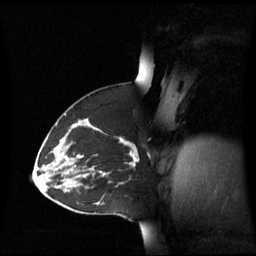
Breast MRI (dynamic contrast-enhanced), one sagittal slice. Slice 37 of 60 in the series (ordered by position). Dynamic contrast-enhanced series, image 2 of 3 at this slice position (ordered by acquisition). 1.5 T. TE 4.2 ms, TR 8.4 ms. 2.8 mm slice thickness. 256 × 256 image matrix, field of view 270 × 270 mm. Patient: female, 43 years. Case-level facts recorded for this patient, not image findings: setting: breast cancer imaged before/during neoadjuvant chemotherapy; receptor status: triple-negative.
Structures marked on this image (semi-automatically segmented with operator editing):
- analysis volume of interest (the breast-tissue region the enhancement analysis was run in; not a lesion): box from (x=55, y=124) to (x=139, y=173) px
- tumour enhancement mask (voxels above the 70 % enhancement threshold inside the analysis volume of interest): (x=58, y=137)–(x=139, y=173)